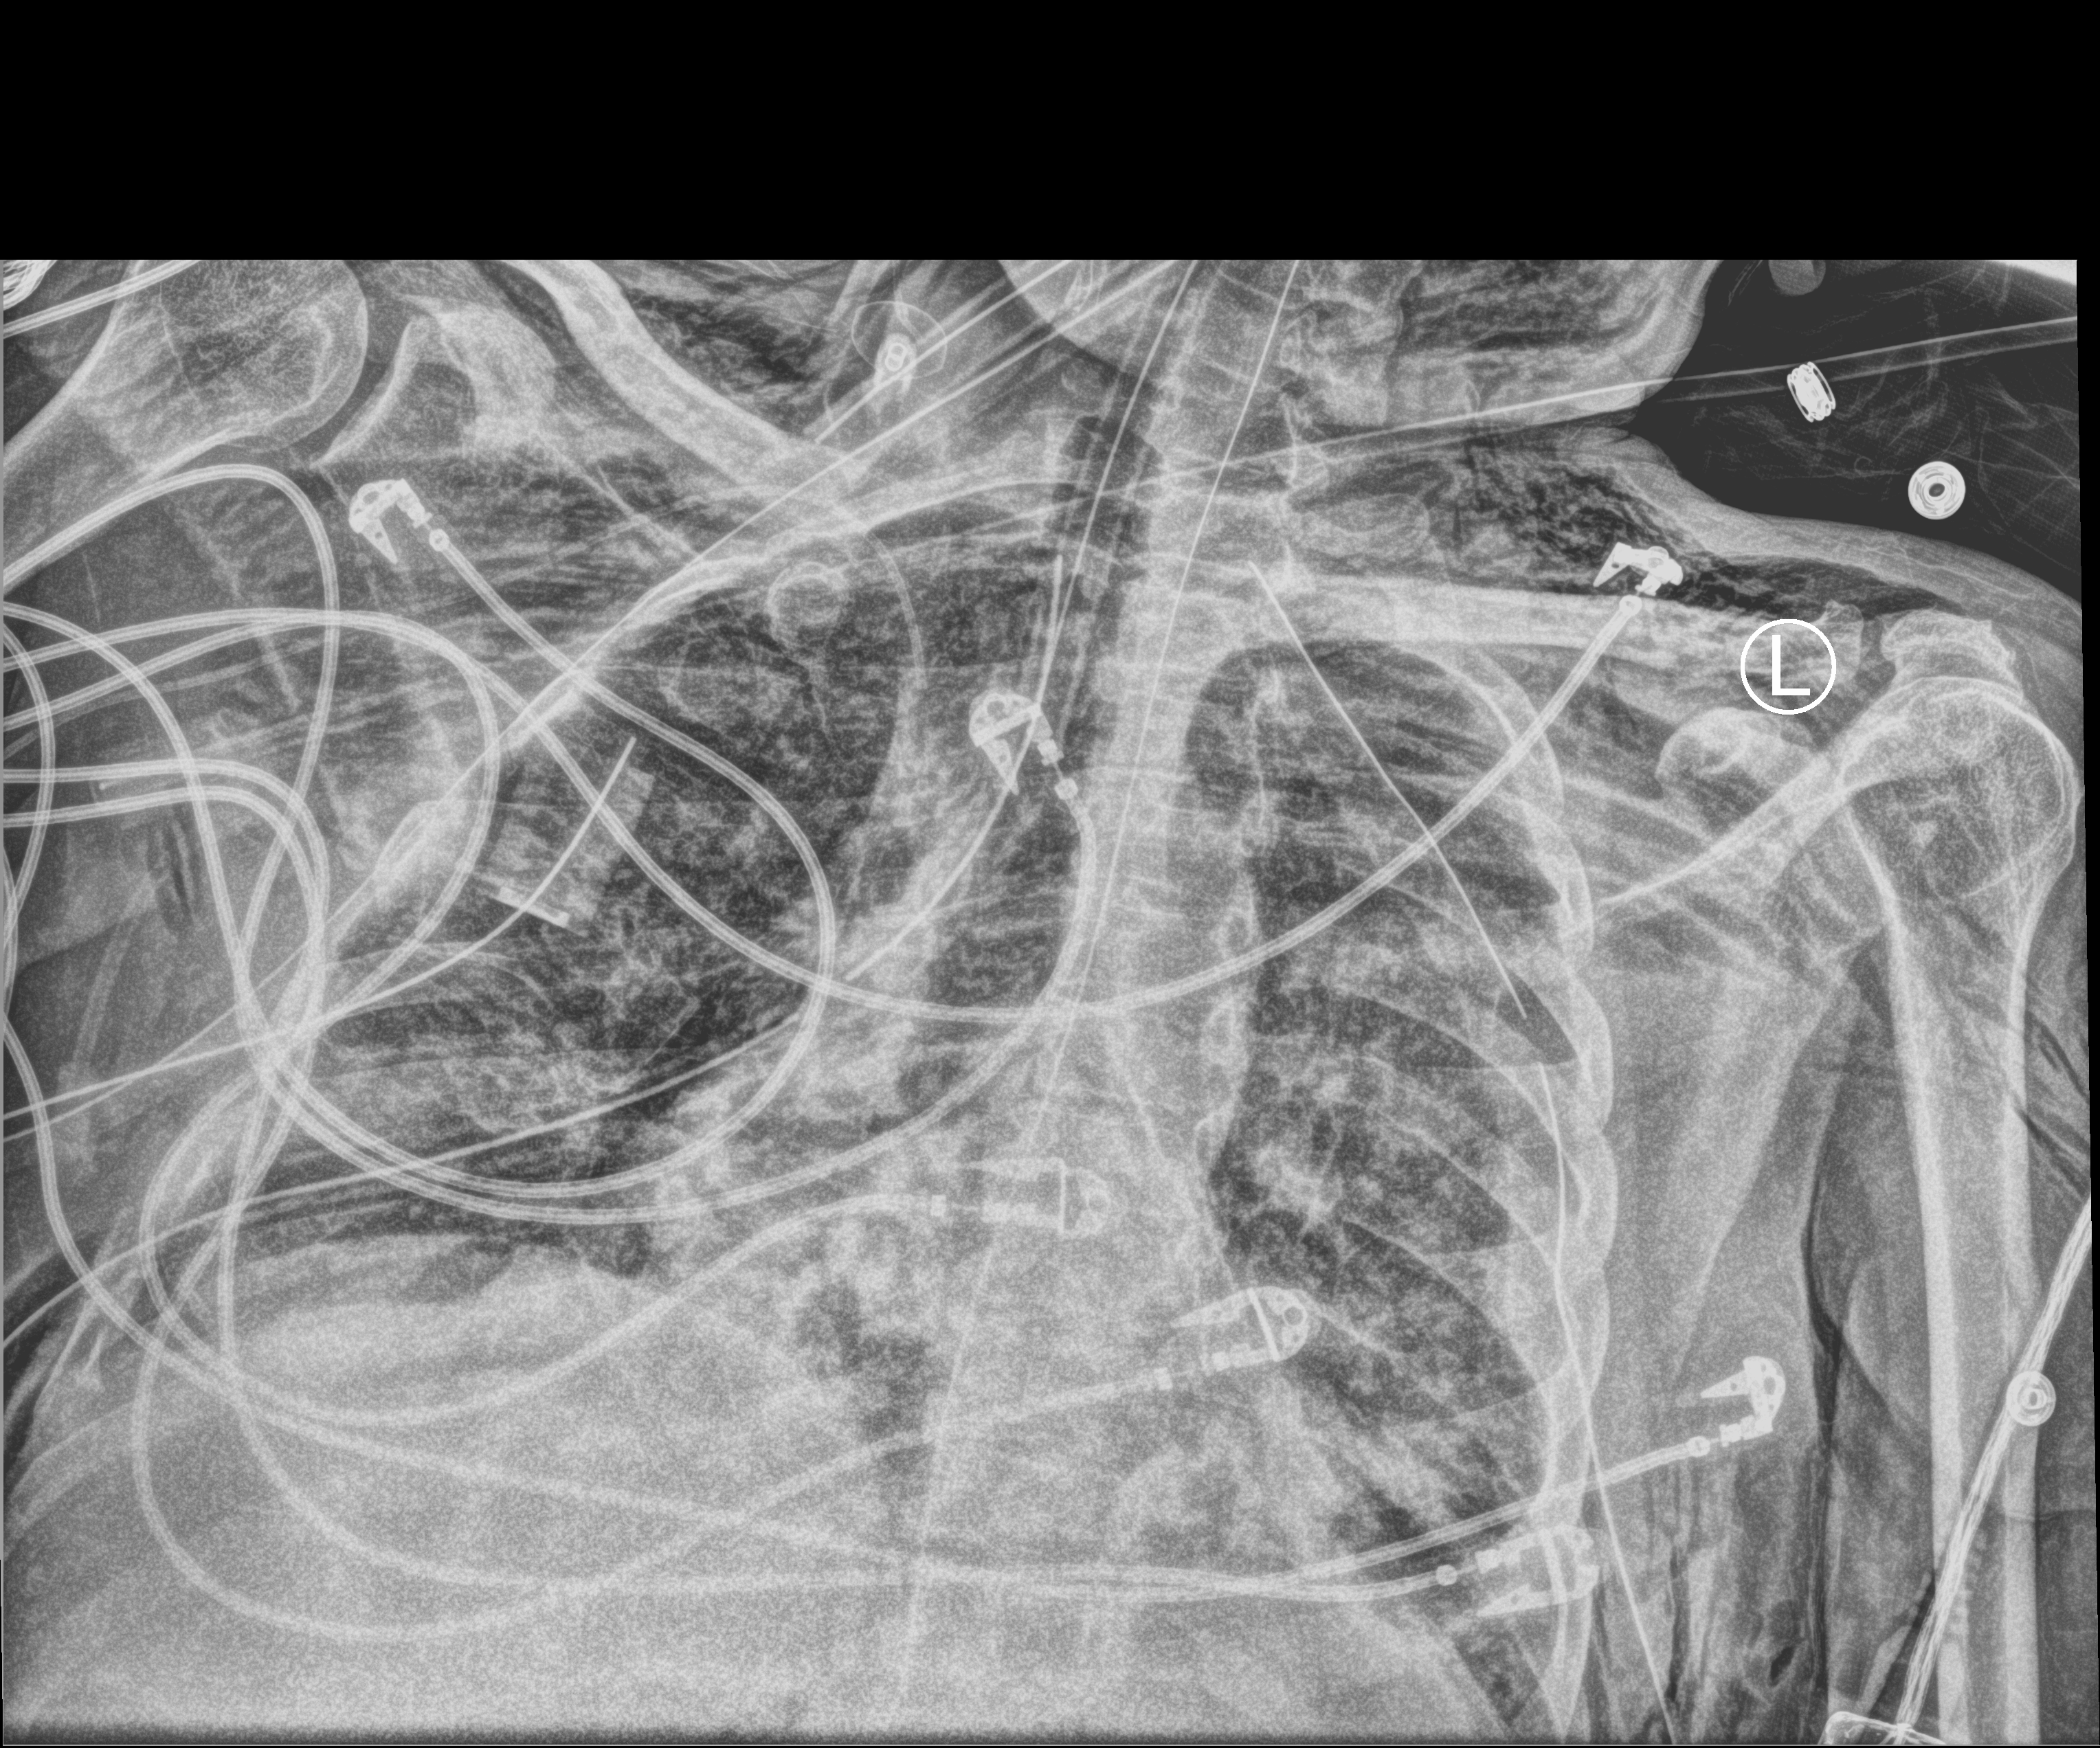
Bedside chest radiograph (computed radiography); anteroposterior (AP) projection. Patient hospitalised with COVID-19; male, aged 18–59 years.
Admission-level facts for this patient (not findings on this image; timing relative to this image not recorded): diabetes (admission record): no; COPD (admission record): no; mechanically ventilated during this hospital stay: yes.